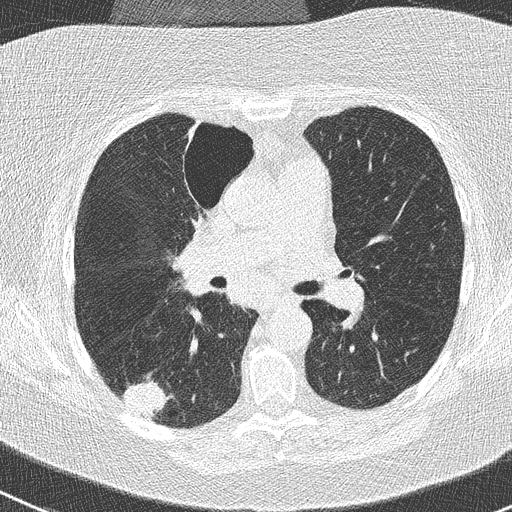
Chest CT (low-dose screening protocol), one axial image, first (baseline) screen, lung window (W 1500 / L -600 HU), 2 mm slice thickness, lung (sharp) reconstruction kernel (B50f), slice 111 of 261 in the series, 512 × 512 image matrix, field of view 310 × 310 mm. Female participant, aged 74 years at enrolment. Former smoker at enrolment.
Expert reader's lesion annotation, bounding box (x1, y1, x2, y2) in pixels: (117, 377, 173, 427). The screening reader recorded 3 non-calcified nodules or masses ≥4 mm on this exam (right lower lobe, right upper lobe, left lower lobe); which of them this box marks is not recorded. Participant outcome: lung cancer diagnosed 16 days after this screen — non-small cell carcinoma, right lower lobe, poorly differentiated (G3), stage IIIA (AJCC 6th edition), 28 mm at pathology.